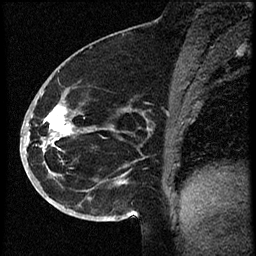
Breast MRI (dynamic contrast-enhanced), one sagittal slice; position 31 of 60 along the scan axis; dynamic contrast-enhanced study with each time point stored as its own series, time point 2 of 3 at this slice position (early post-contrast, ordered by acquisition time); 1.5 T; TE 4.2 ms, TR 18.9 ms; 256 × 256 image matrix. Female patient. From the clinical record (not read from this slice): setting: breast cancer imaged before/during neoadjuvant chemotherapy; receptor status: HR-positive, HER2-negative.
Structures marked on this image (semi-automatically segmented with operator editing):
- analysis volume of interest (the breast-tissue region the enhancement analysis was run in; not a lesion): bounding box (x1, y1, x2, y2) in pixels: (30, 87, 114, 173)
- tumour enhancement mask (voxels above the 100 % enhancement threshold inside the analysis volume of interest): (42, 105, 73, 151)